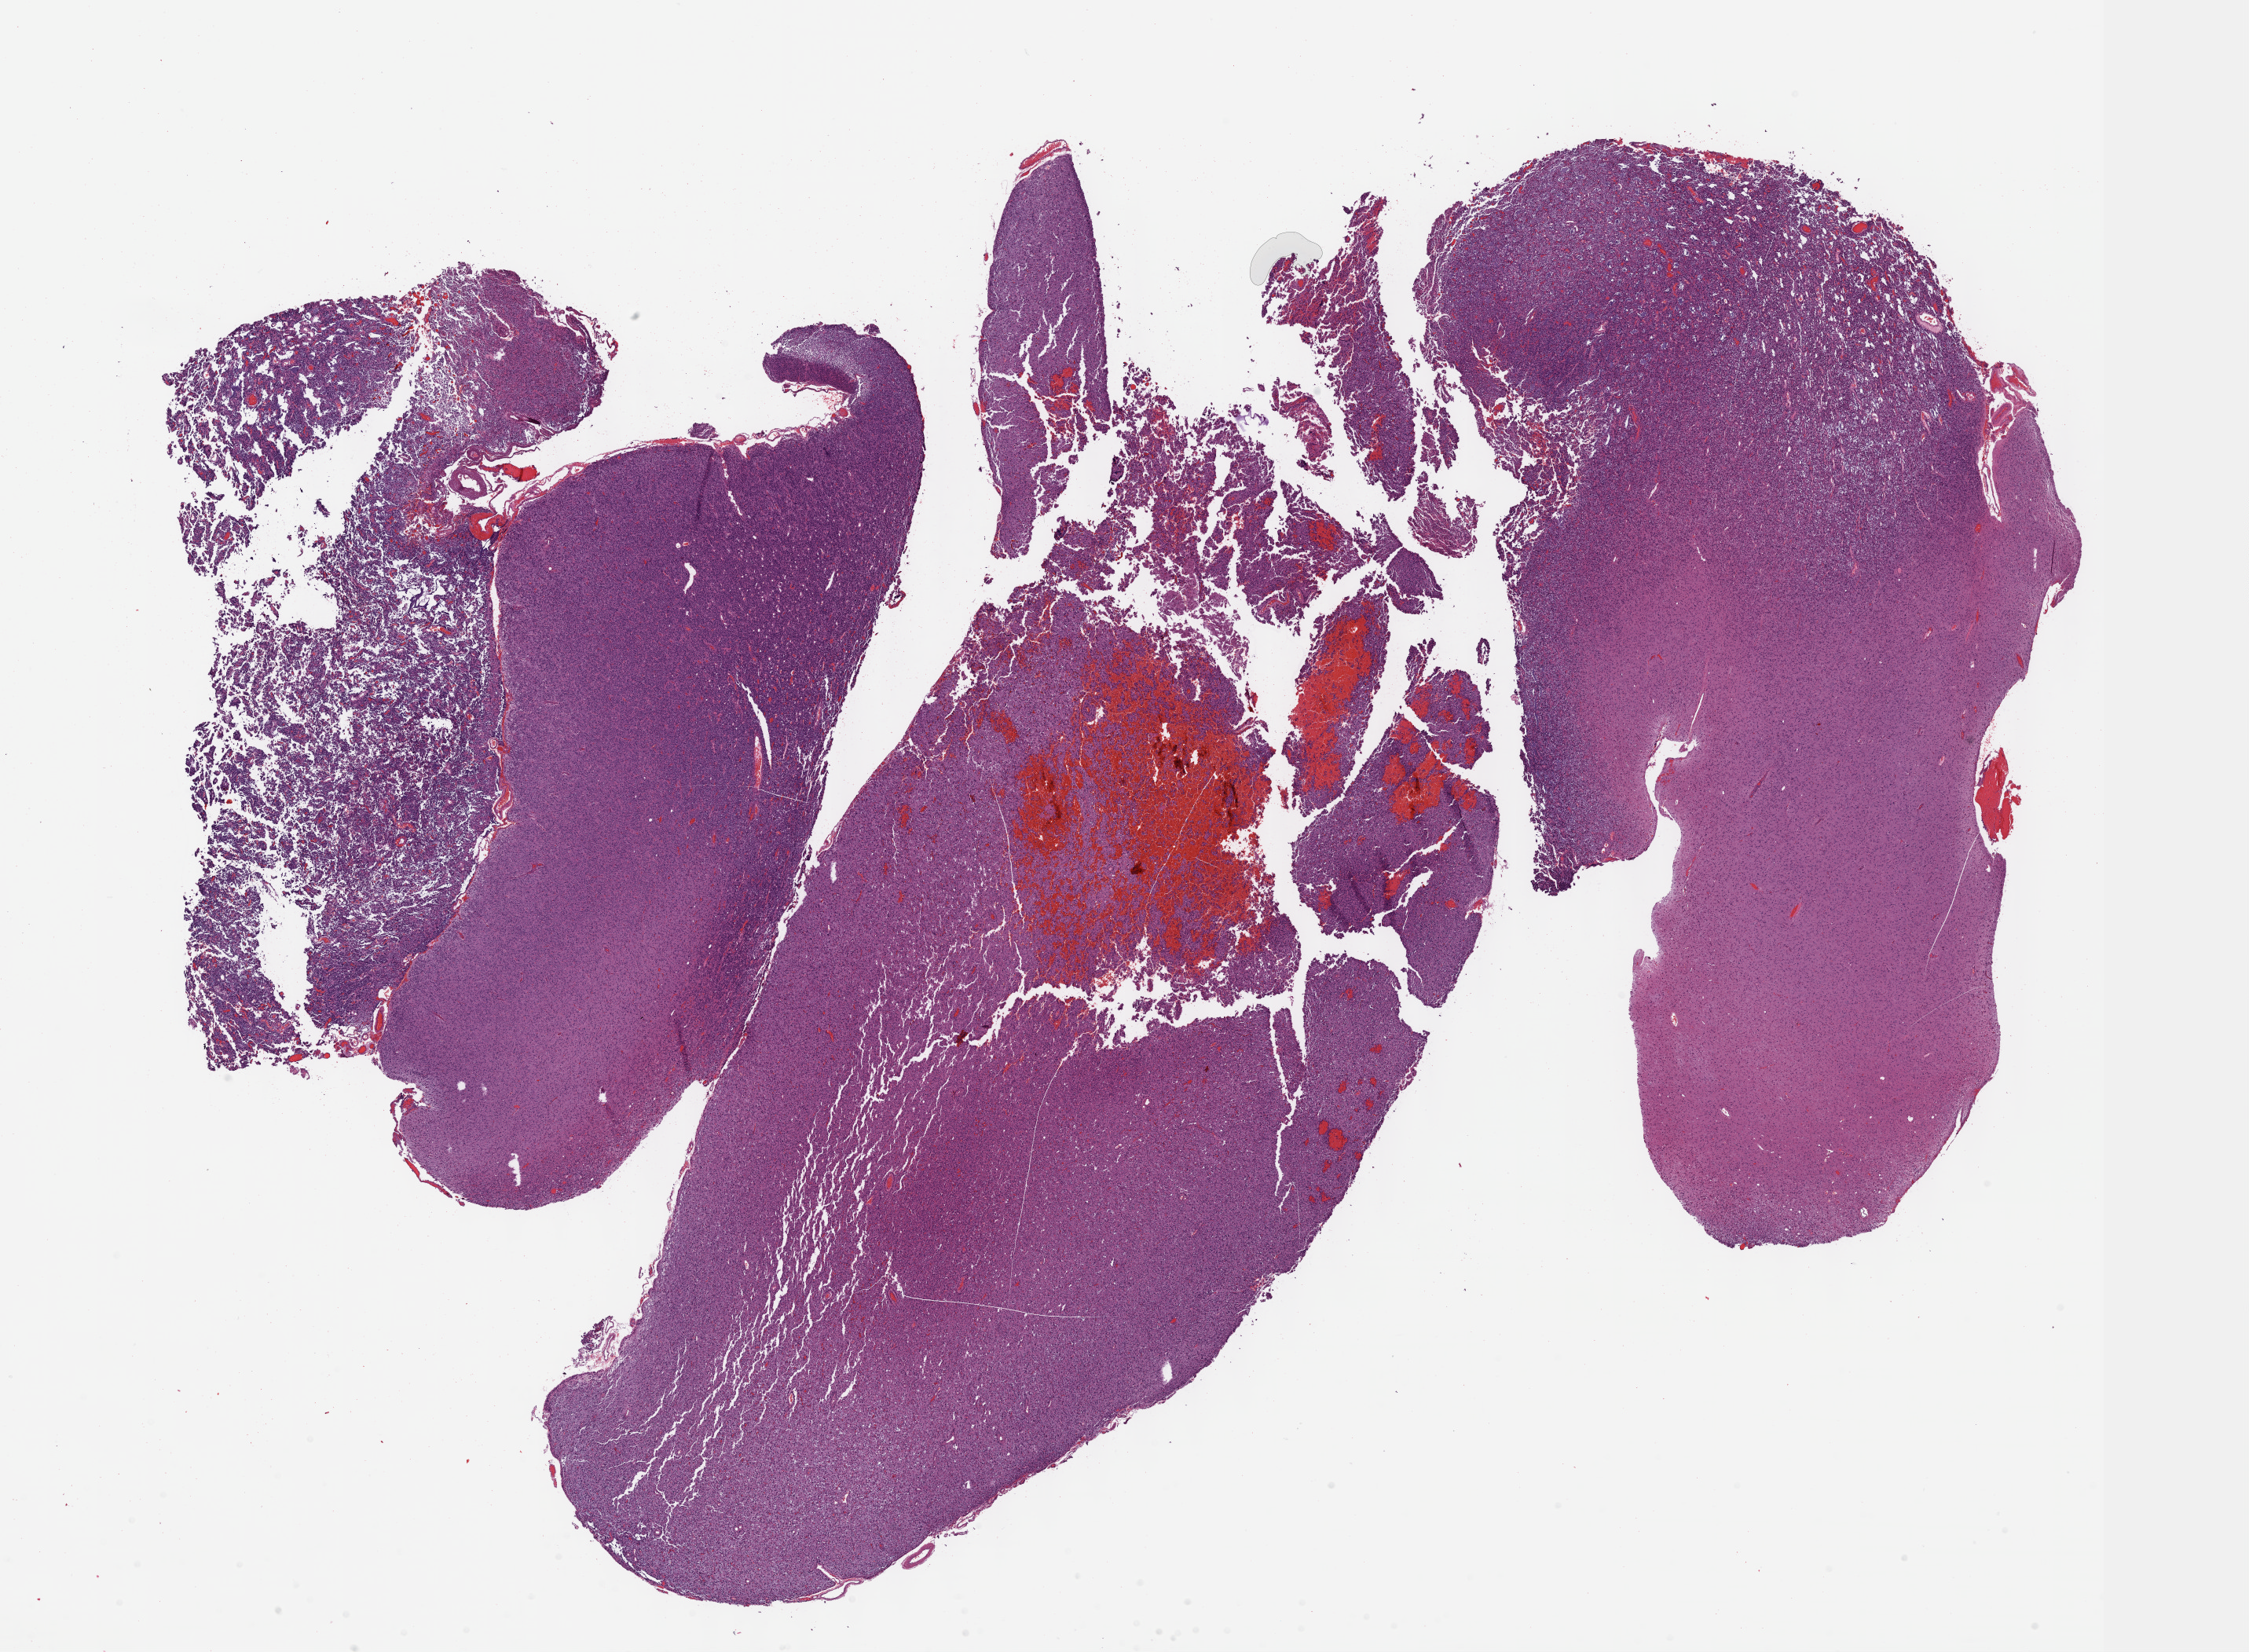
Whole-slide histology image, H&E-stained — whole scanned area (about 23.1 x 17.0 mm) shown as a low-resolution overview. Formalin-fixed paraffin-embedded (FFPE) diagnostic section. Brain, primary tumour sample. Male patient; age at initial diagnosis 59 years. Histologic grade: G3 (poorly differentiated).
Histologic diagnosis: Oligodendroglioma, anaplastic (cerebrum). Laterality: left.